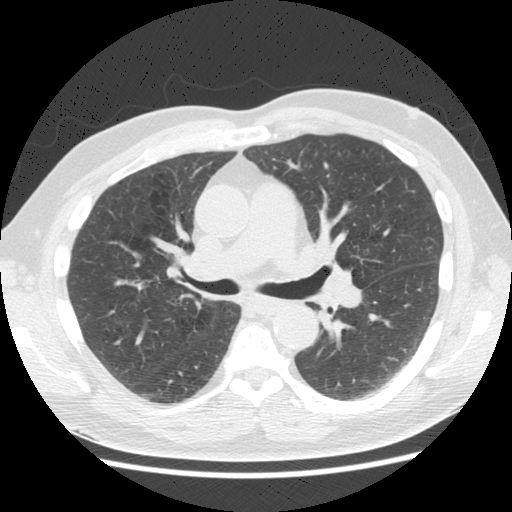
Low-dose screening chest CT, one axial slice; position 99 of 161 along the scan axis; reconstruction kernel STANDARD; 120 kVp; lung window (W 1500 / L -600 HU); 2.5 mm slice thickness; 512 × 512 image matrix, field of view 360 × 360 mm.
Outlined on this slice (manually delineated by an expert):
- lesion 1 (tumor, upper lobe of right lung): bounding box [x1, y1, x2, y2] px = [134, 296, 144, 302]